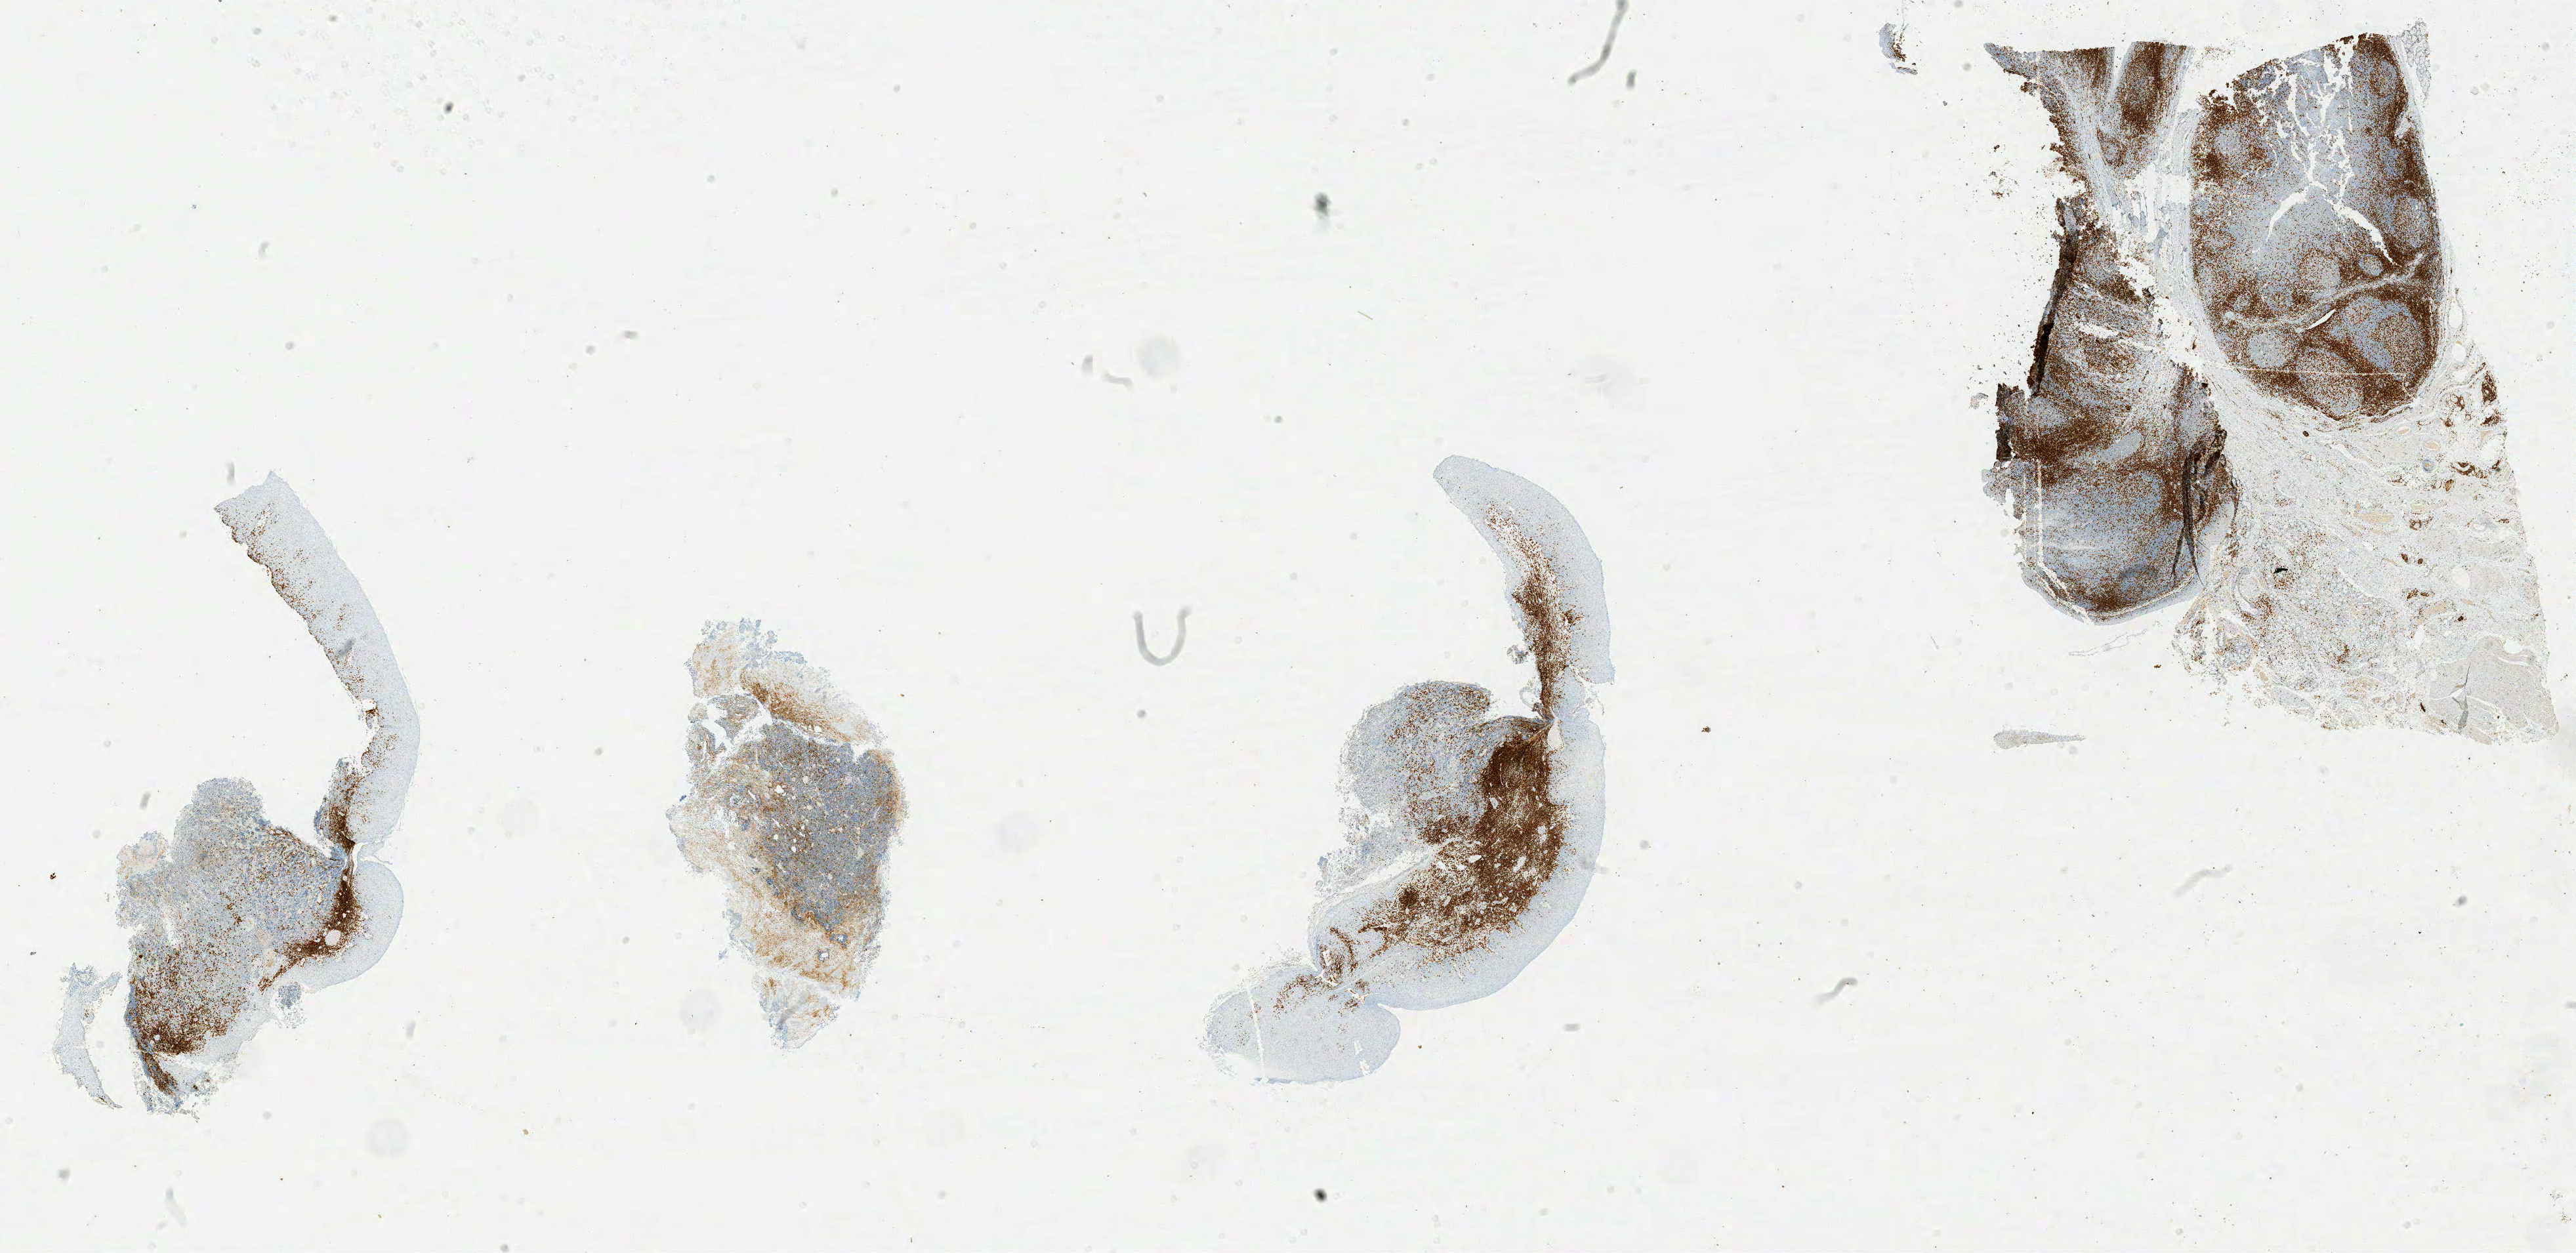
Immunohistochemistry (IHC) whole-slide image stained for CD3, shown as a low-resolution overview of the whole scanned area (about 31.3 x 15.2 mm), specimen: tumor tissue. Patient male; 66 years old.
- diagnosis: Burkitt lymphoma, NOS